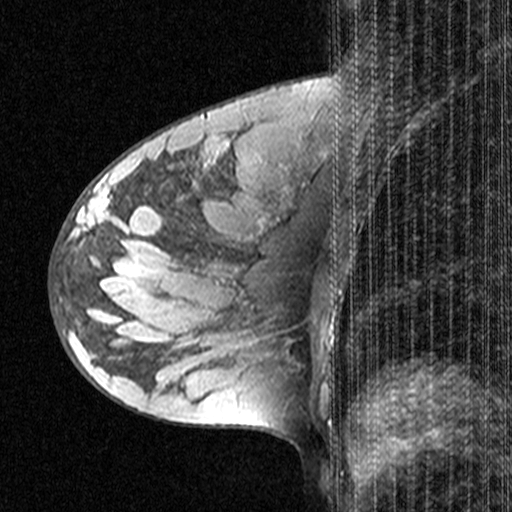
Breast MRI (dynamic contrast-enhanced), one sagittal slice. Position 19 of 44 along the scan axis. Dynamic contrast-enhanced study with each time point stored as its own series, time point 2 of 3 at this slice position (early post-contrast, ordered by acquisition time). 1.5 T. TE 4.5 ms, TR 11 ms. 3 mm slice thickness. 512 × 512 image matrix, field of view 200 × 200 mm. Patient: female, 28 years. Case-level facts recorded for this patient, not image findings: setting: breast cancer imaged before/during neoadjuvant chemotherapy; receptor status: HR-positive, HER2-negative.
Outlined on this slice (semi-automatically segmented with operator editing):
- analysis volume of interest (the breast-tissue region the enhancement analysis was run in; not a lesion): bounding box (x1, y1, x2, y2) in pixels: (49, 182, 151, 283)
- tumour enhancement mask (voxels above the 90 % enhancement threshold inside the analysis volume of interest): (79, 182, 101, 214)